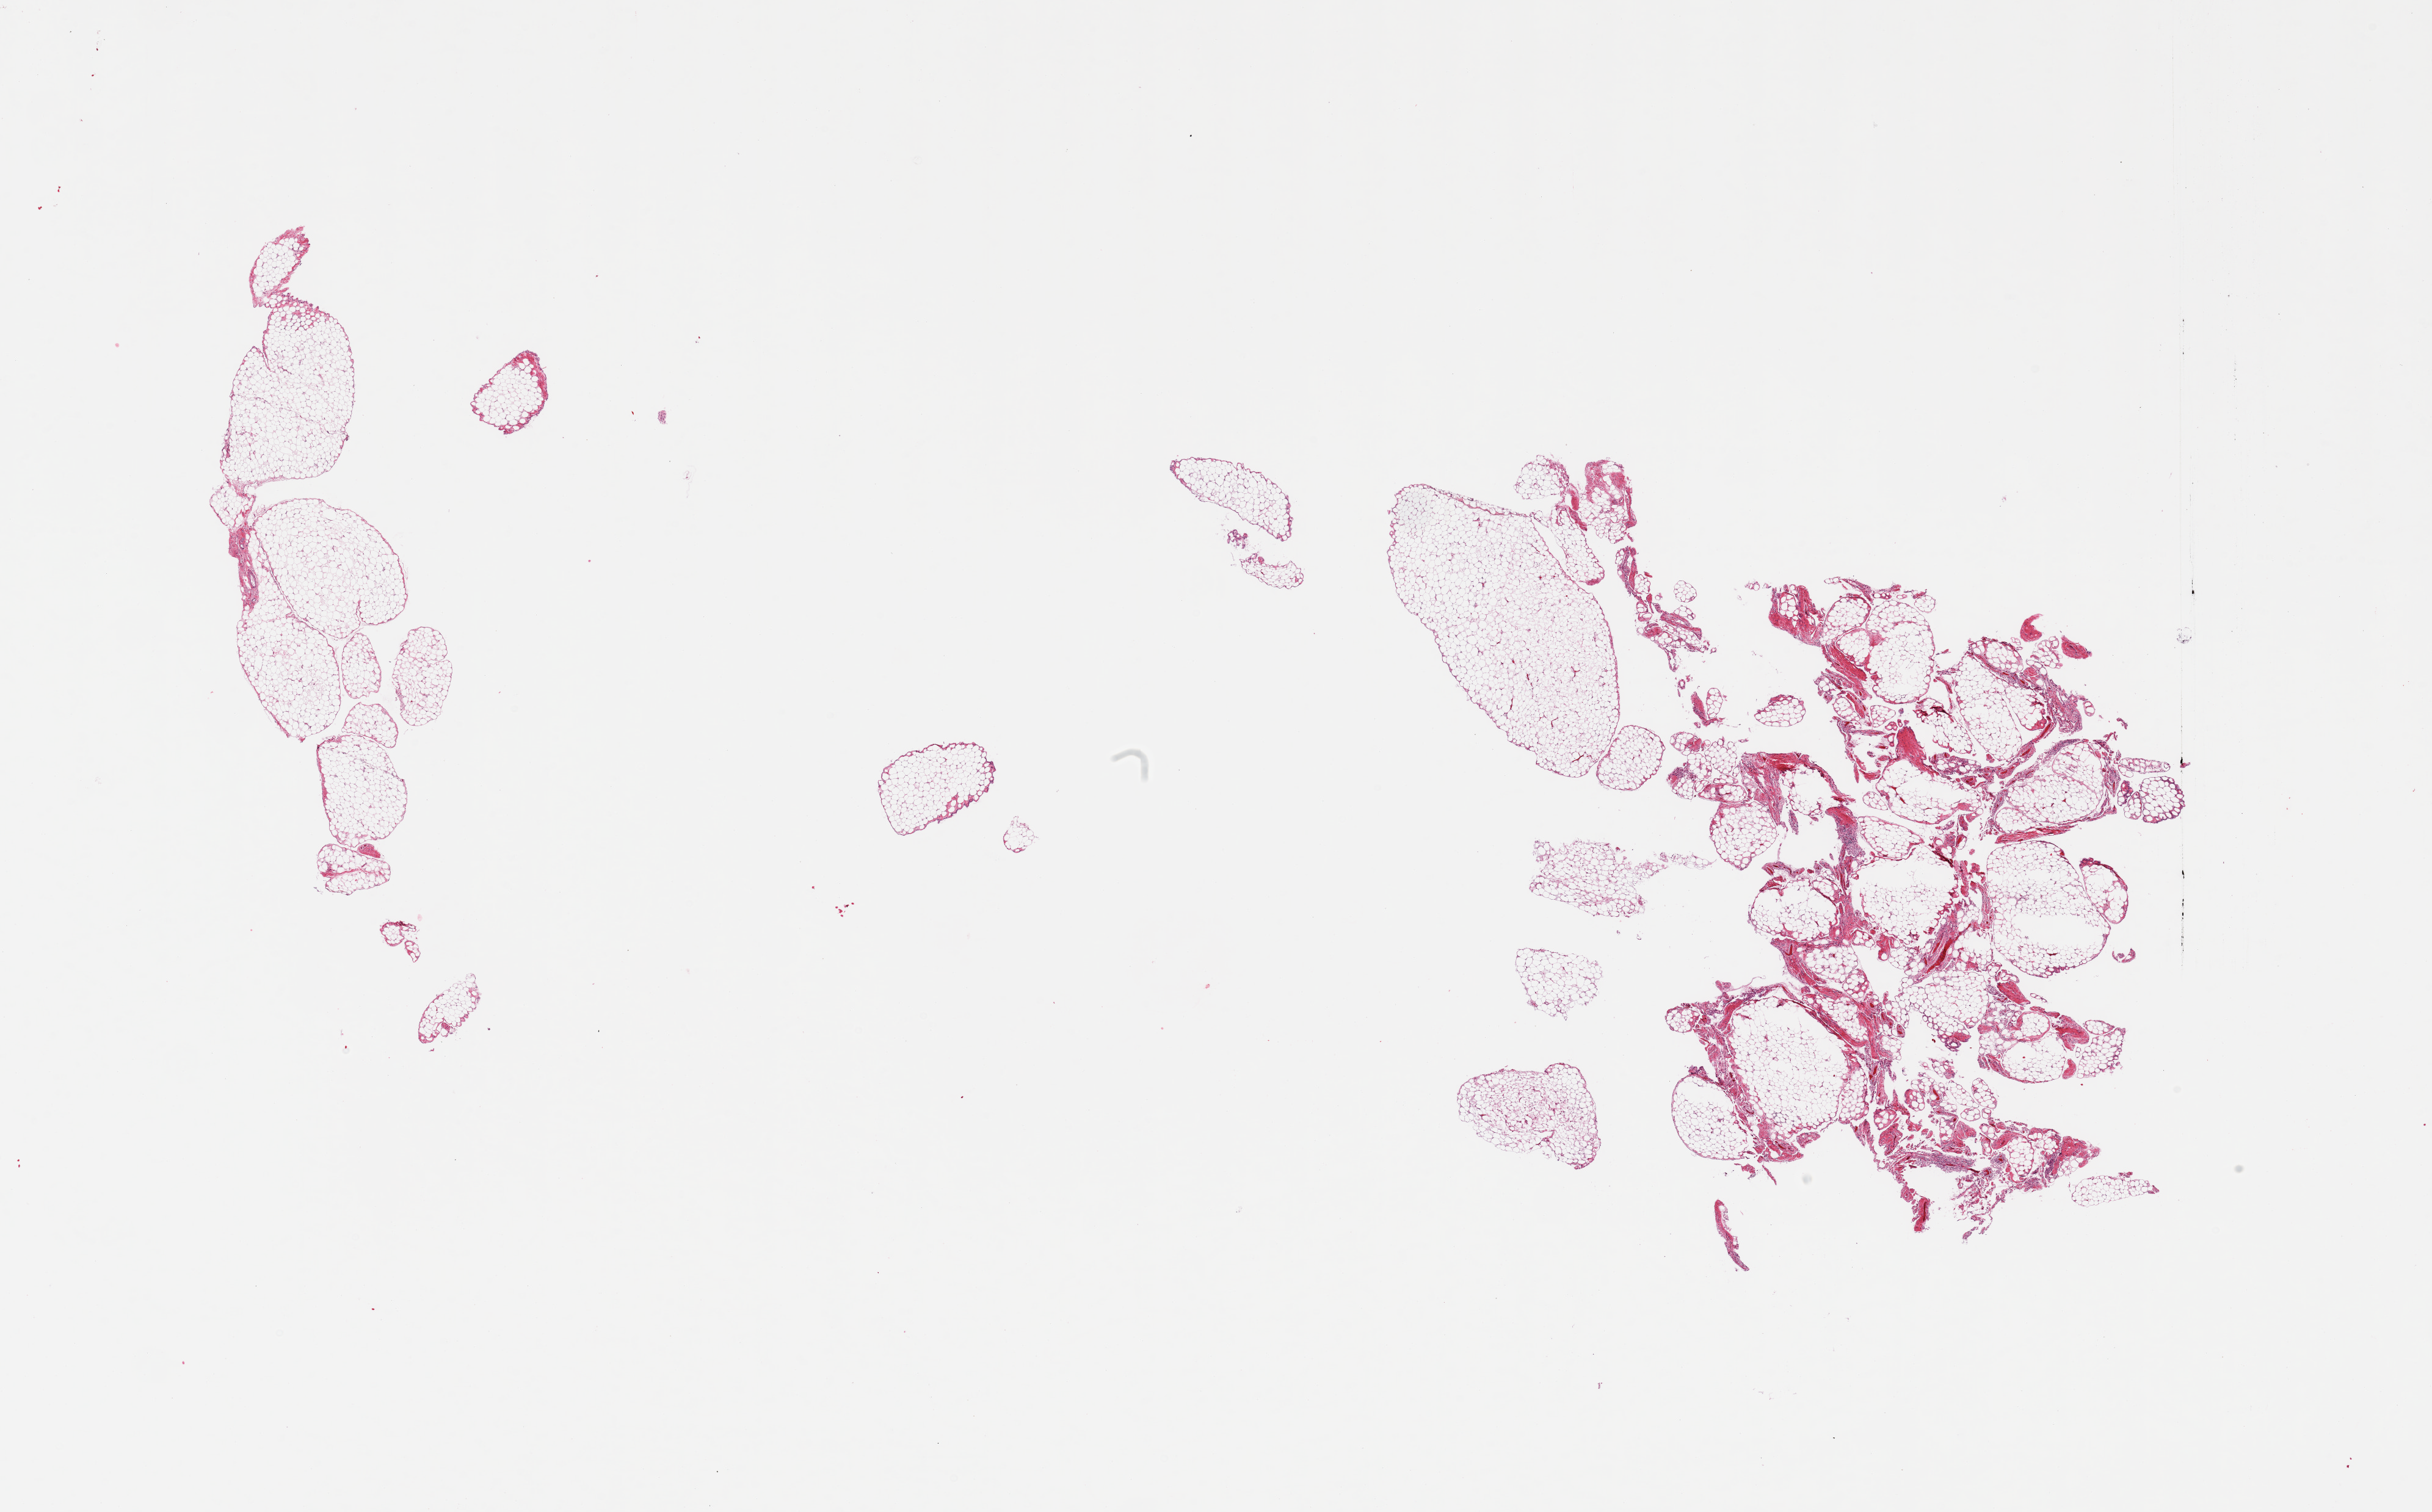
Whole-slide image, H&E stain — shown as a low-resolution overview of the whole scanned area (about 31.5 x 19.6 mm, acquisition: 20x scan), PAXgene-fixed paraffin-embedded (PFPE) section, section of omentum (target tissue), donor tissue sample. Male donor.
Reviewer comment on this tissue sample: 2 partly fragmented pieces; 10% fibrous content in one.